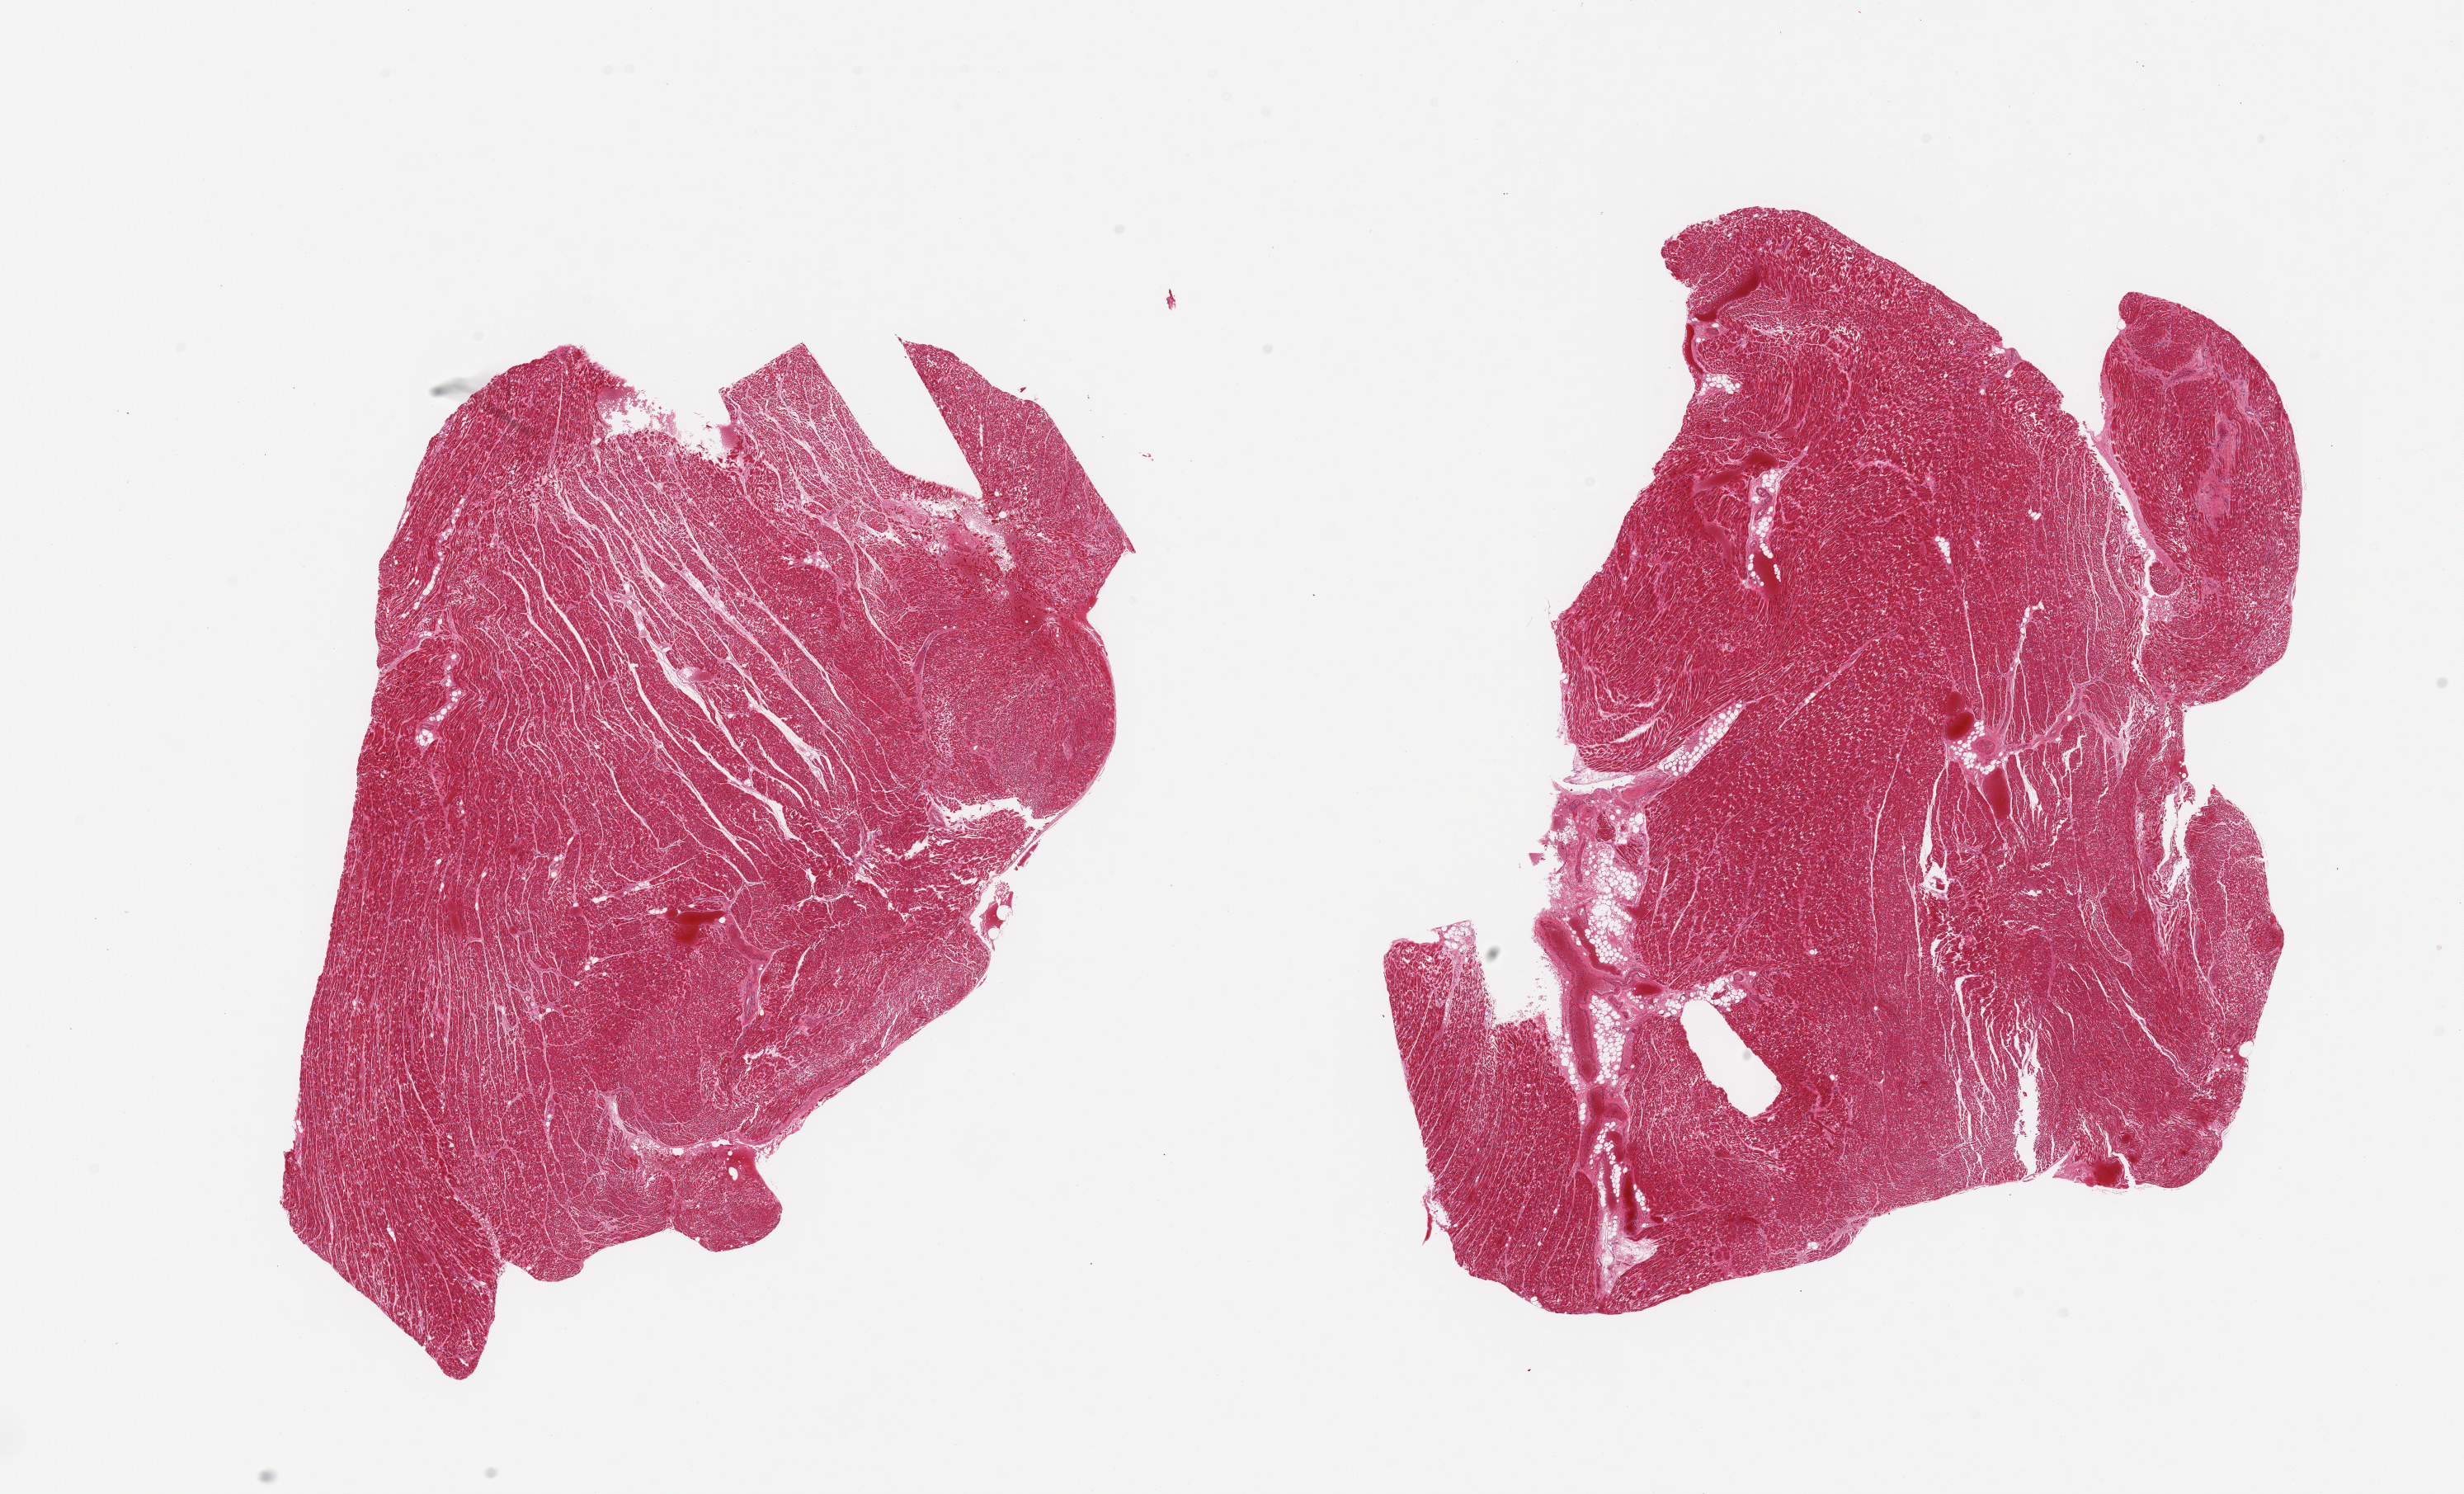
Whole-slide image, H&E stain, brightfield — whole scanned area (about 23.6 x 14.3 mm) shown as a low-resolution overview, PAXgene-fixed, paraffin-embedded tissue, sampled site (target tissue): heart, tissue donor sample. Female donor.
Pathologist's review note for this sample: 2 pieces; myofiber fragmentation; congested vessels.